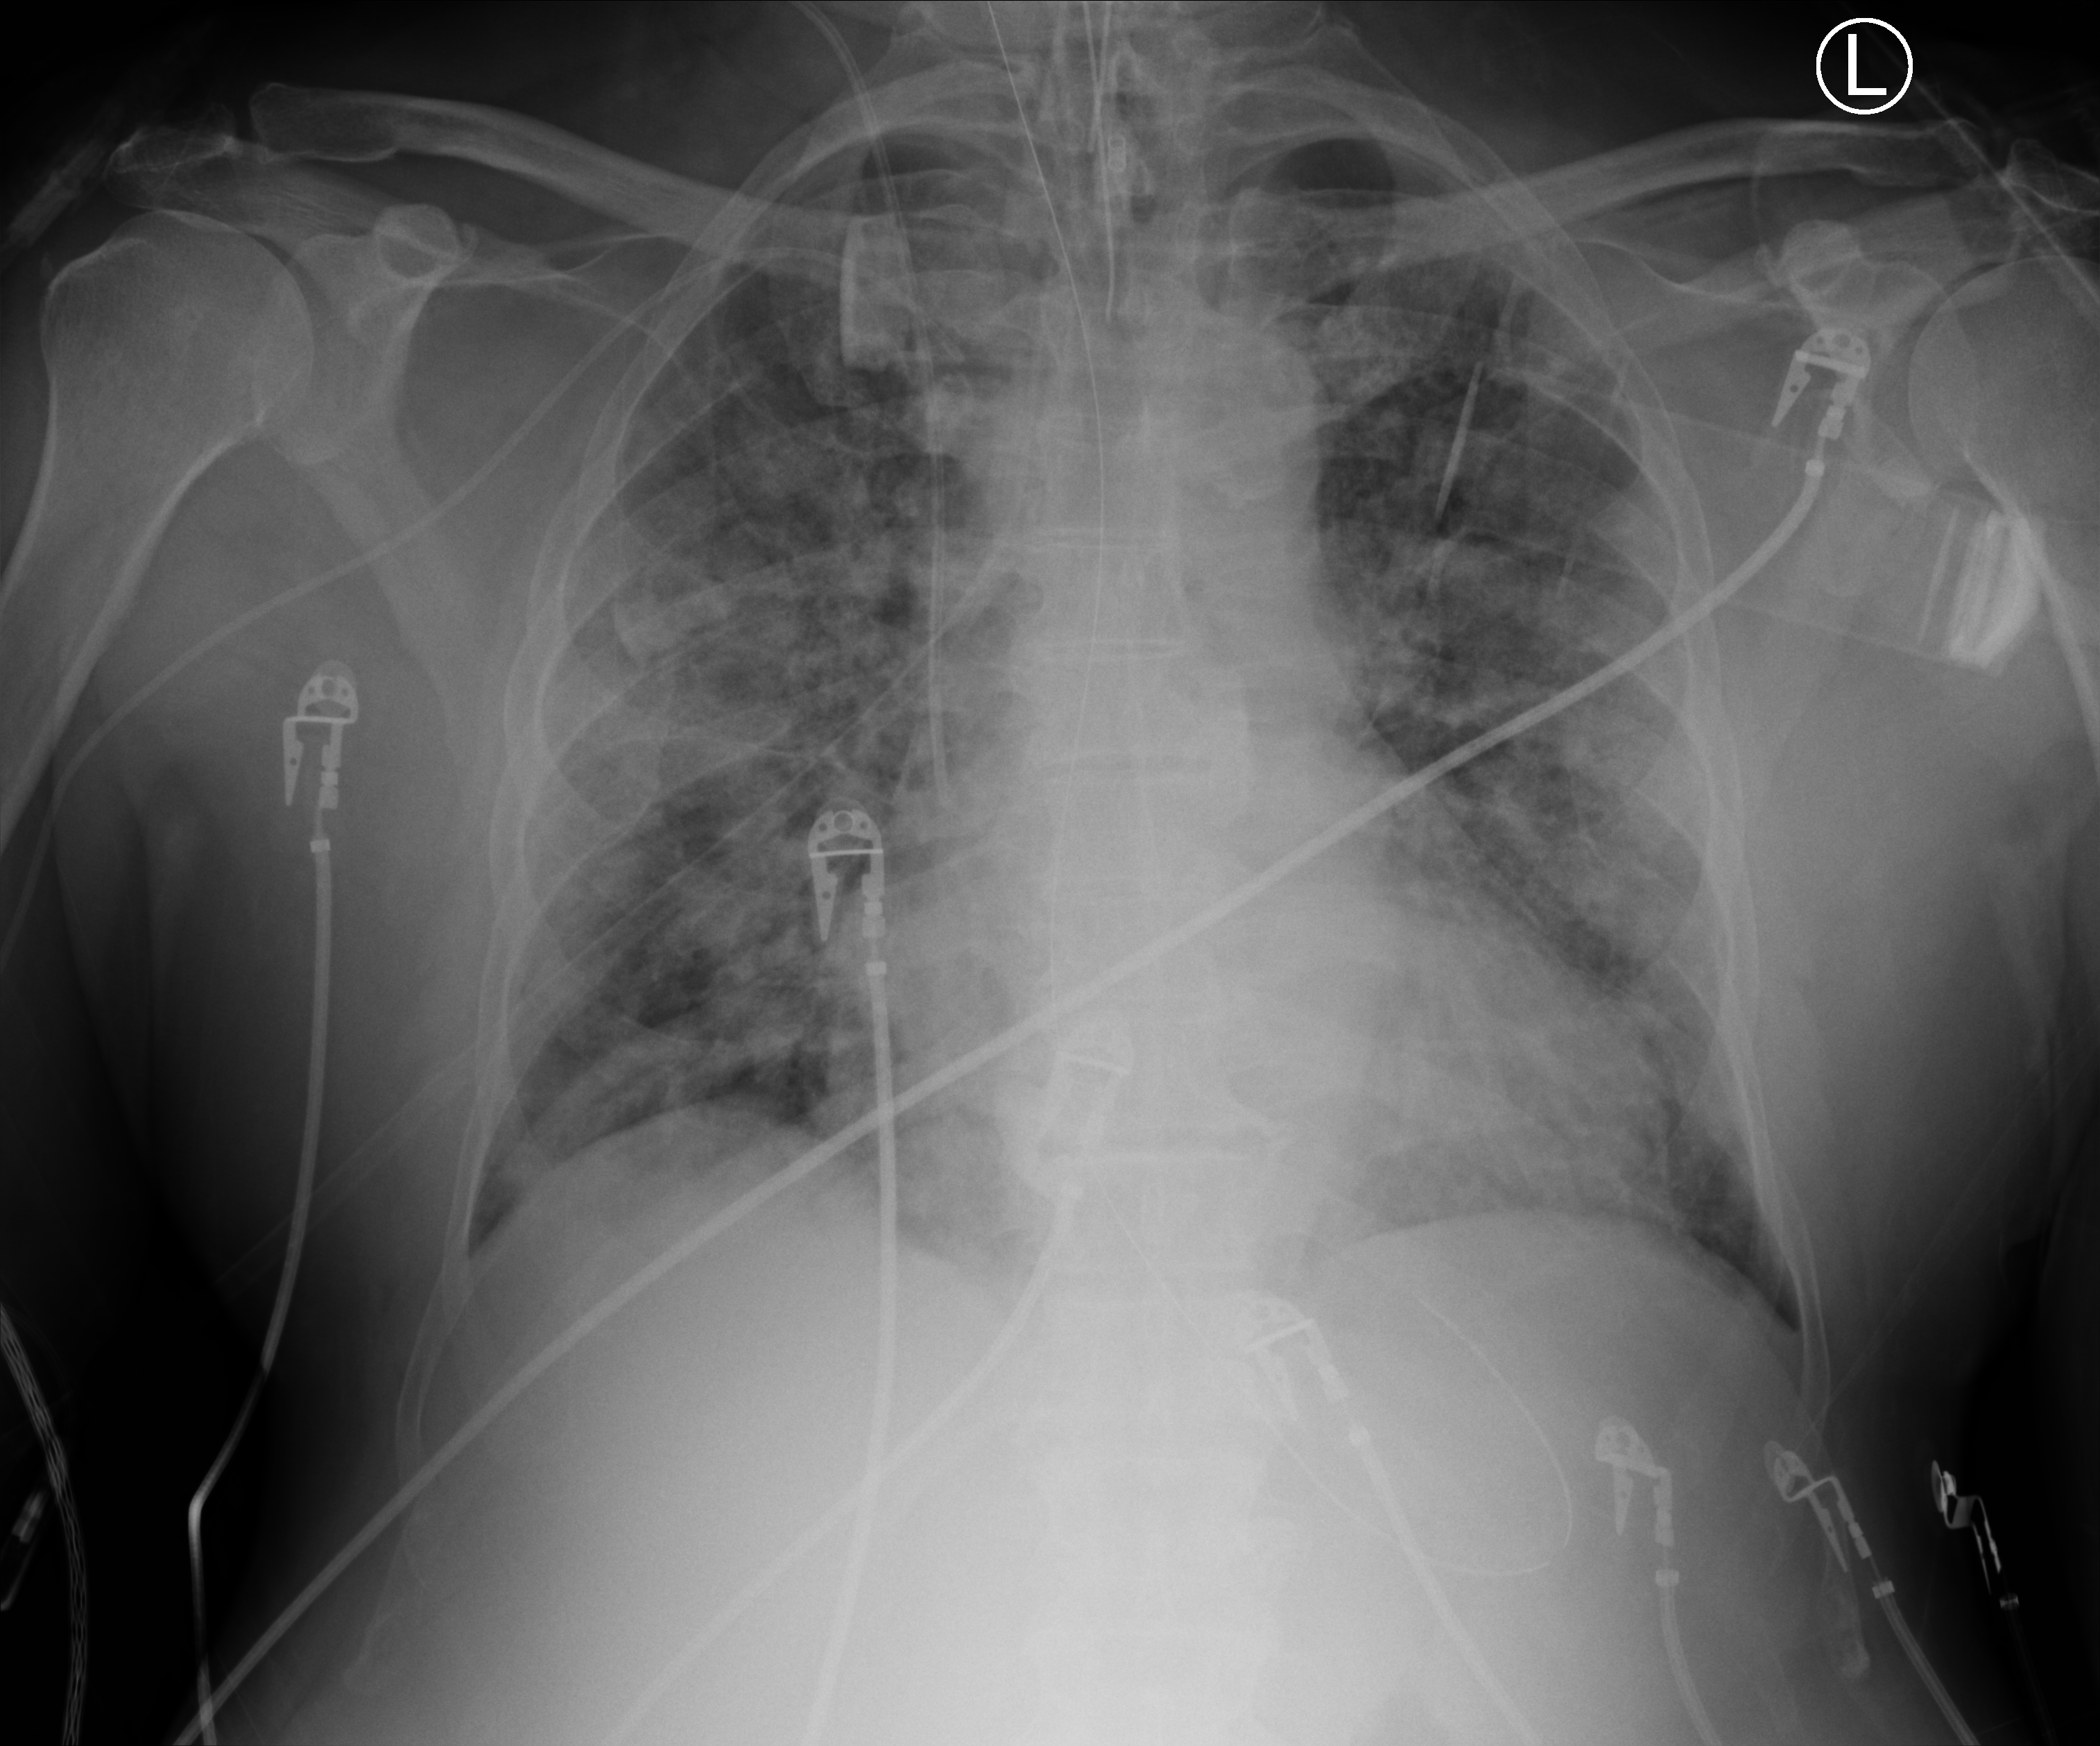
Chest X-ray (portable), anteroposterior (AP) projection. Patient hospitalised with COVID-19; male, aged 60–74 years.
From the hospital-stay record, not from the radiograph (when in the stay this image was taken is not recorded): diabetes (admission record): no; admitted to intensive care during this hospital stay: yes.